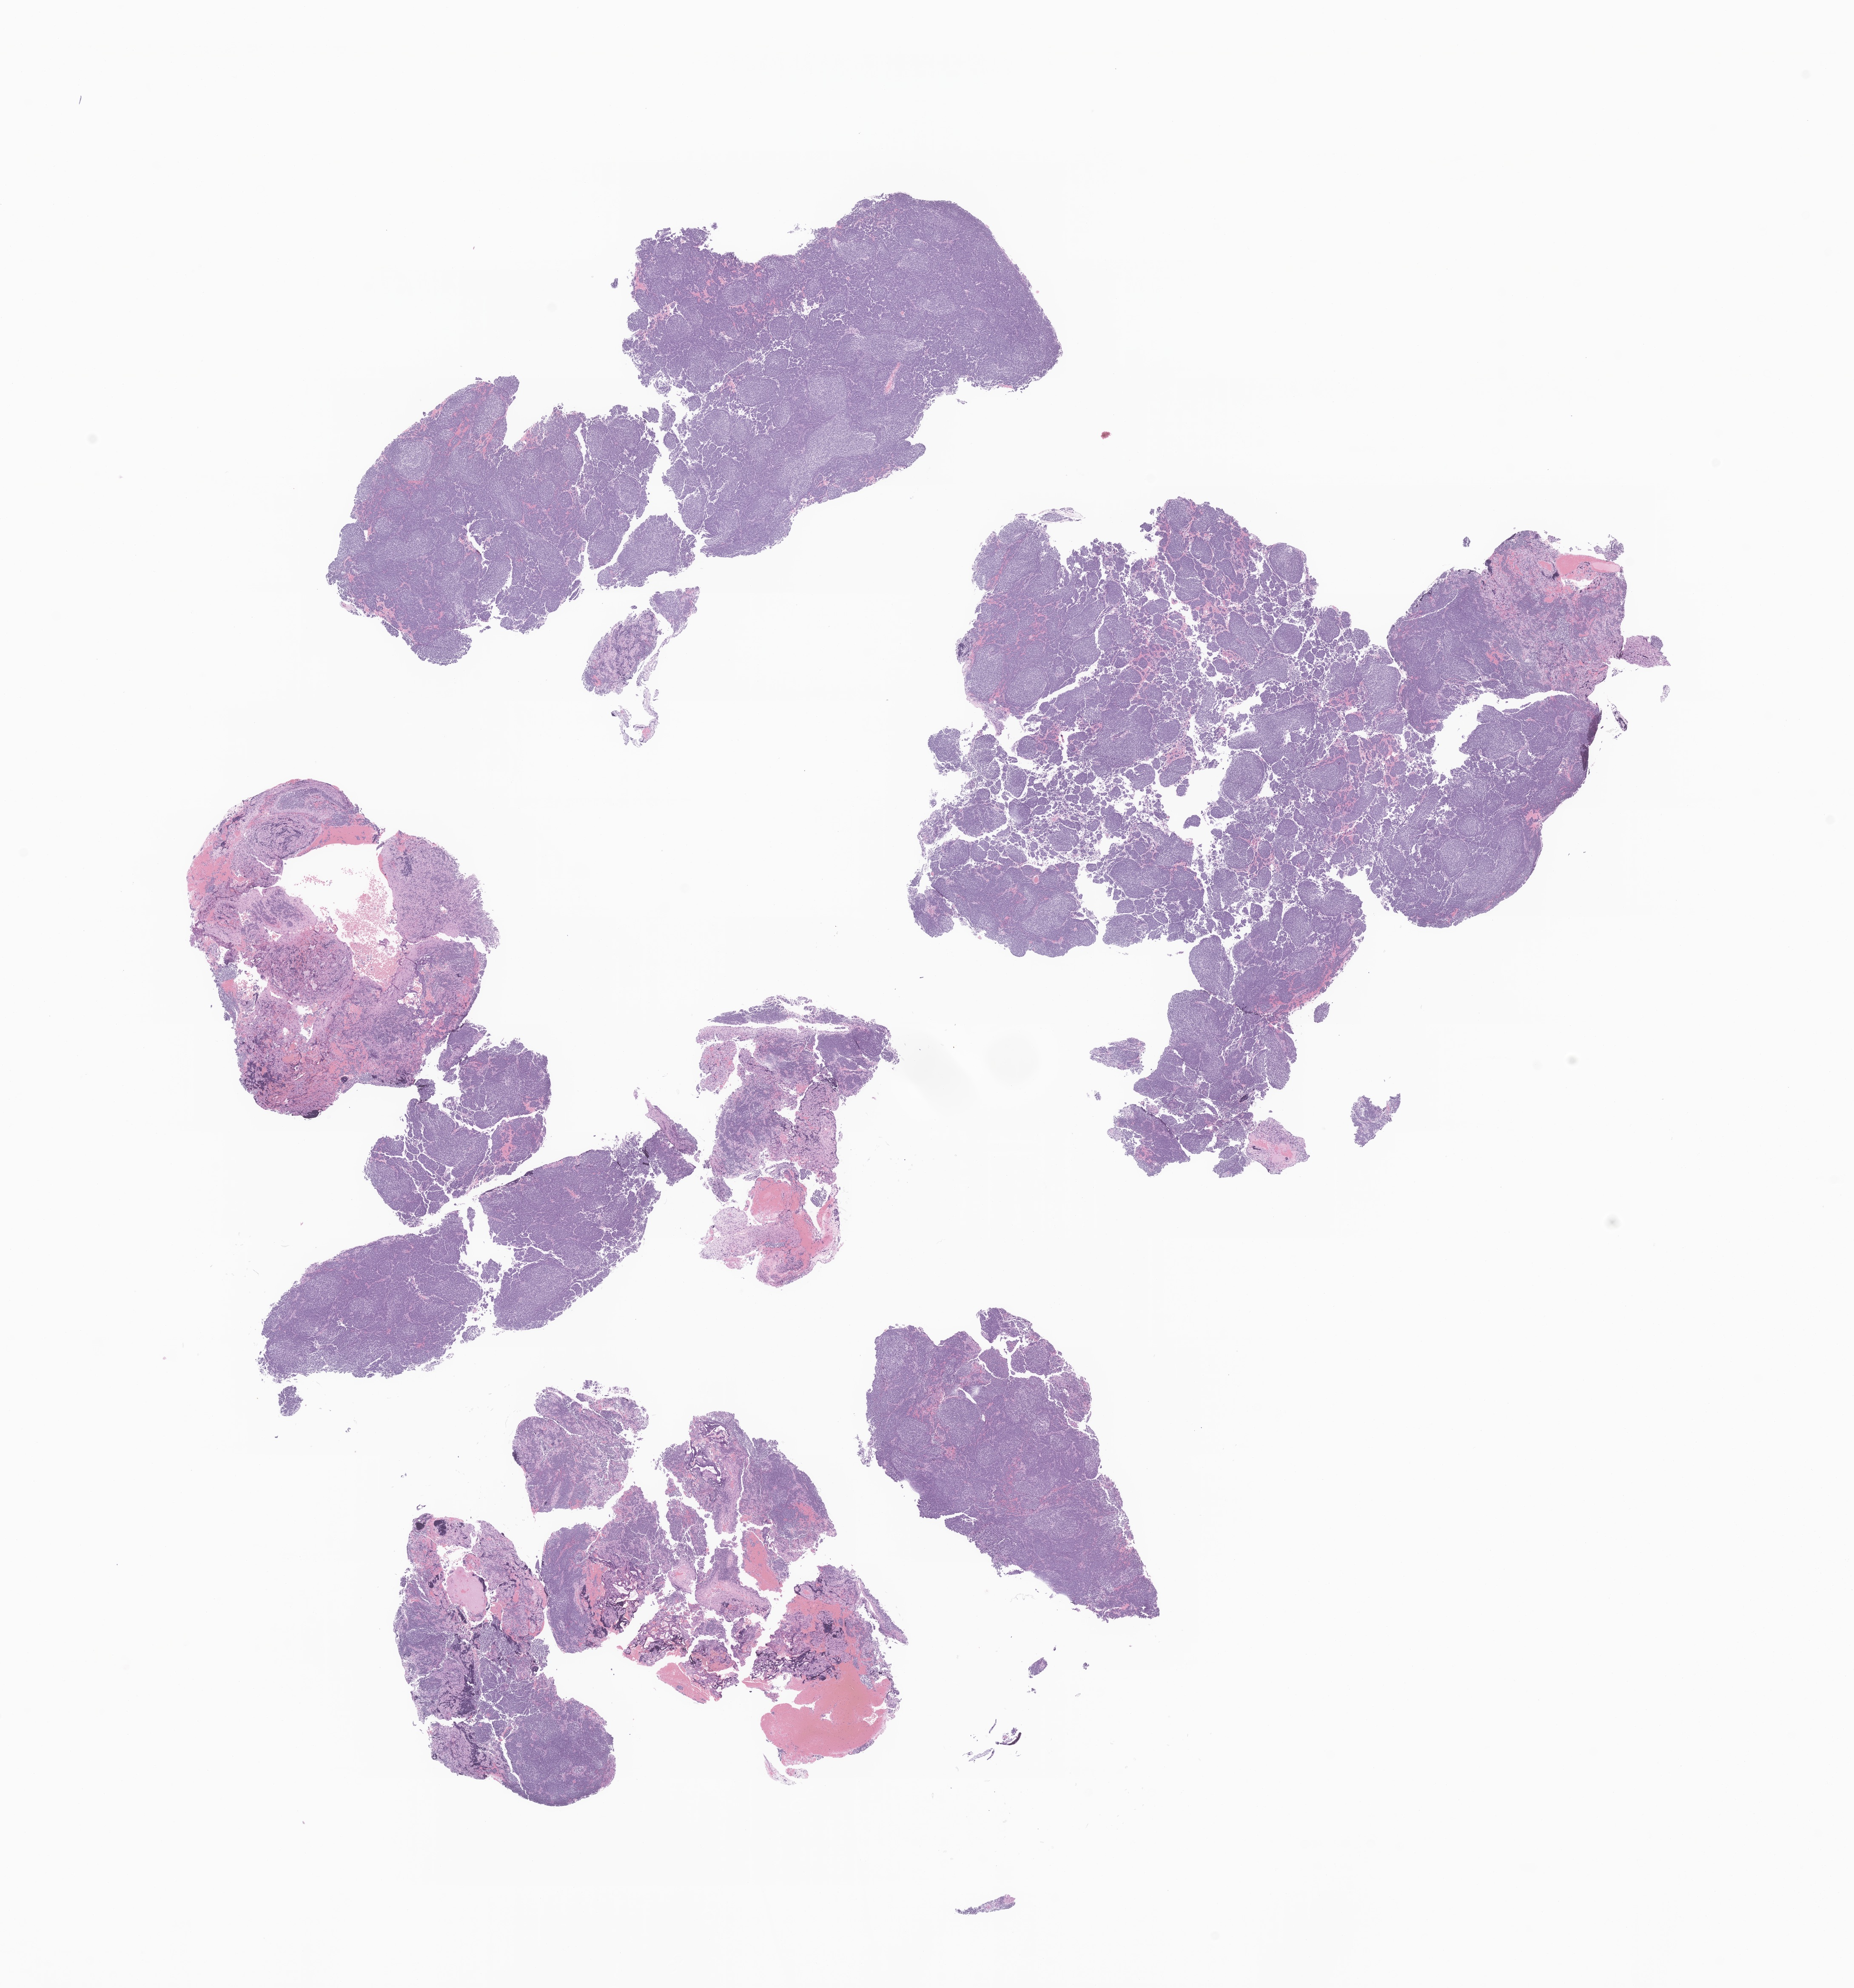
Digitized haematoxylin and eosin-stained section of tumor tissue from the brain, a low-resolution overview of the entire scanned area, about 18.4 x 19.7 mm, formalin-fixed paraffin-embedded section. Patient male; age 127 months (10 years 7 months).
Recorded diagnosis: Medulloblastoma, NOS.